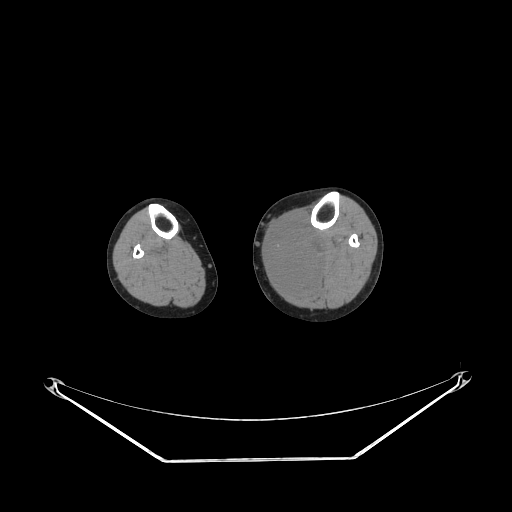
CT of an extremity soft-tissue mass (from a PET/CT study), one axial slice. Slice 142 of 223 in the series (ordered by position). Reconstruction kernel STANDARD. 140 kVp. Soft-tissue window (W 400 / L 40 HU). 3.75 mm slice thickness. 512 × 512 image matrix, field of view 500 × 500 mm. Female patient. From the clinical record (not read from this slice): histological type: extraskeletal high grade osteogenic sarcoma; grade: high; site of the primary tumour: left calf.
Annotated regions visible in this slice (expert contour drawn on MRI and transferred to this co-registered scan by the dataset authors):
- gross tumour volume (mass): bounding box (x1, y1, x2, y2) in pixels: (270, 221, 323, 289)